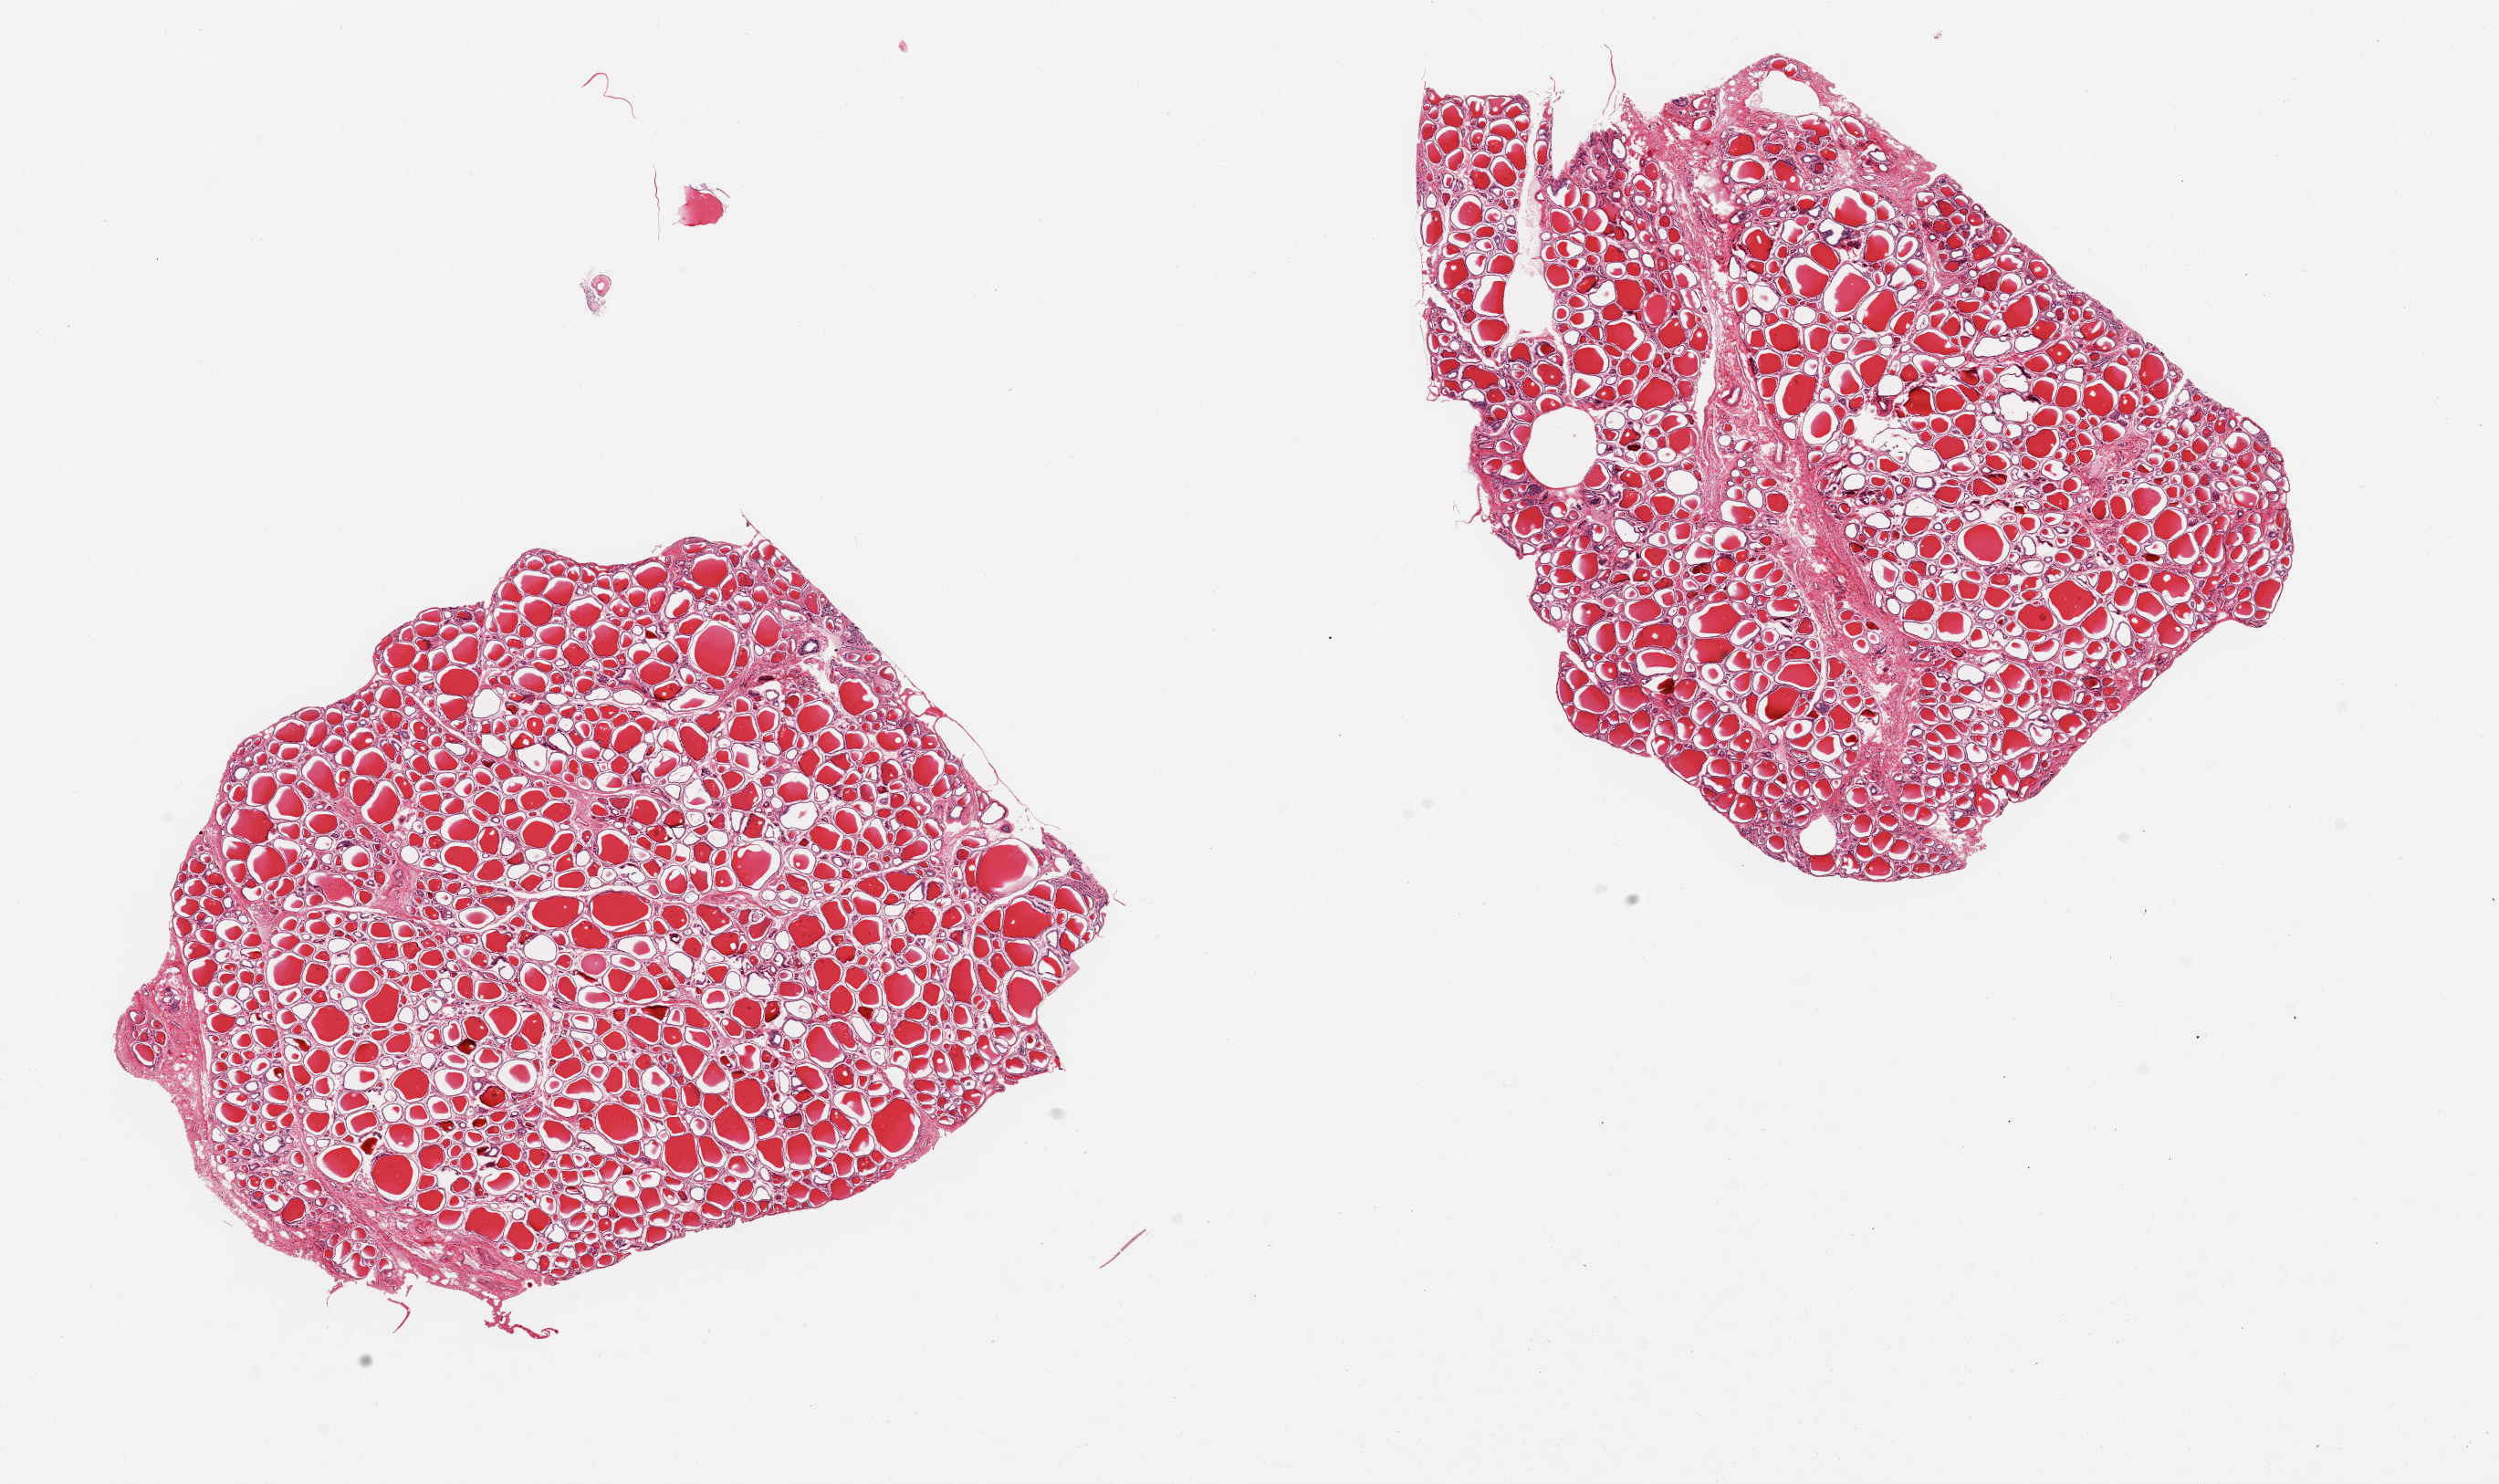
Whole-slide image, H&E stain, brightfield — shown as a low-resolution overview of the whole scanned area (about 21.7 x 12.9 mm, slide scanned at 20x); PAXgene-fixed, paraffin-embedded tissue; sampled site (target tissue): thyroid; donor tissue sample. Donor sex: male.
Pathologist's review note for this sample: 2 pieces.